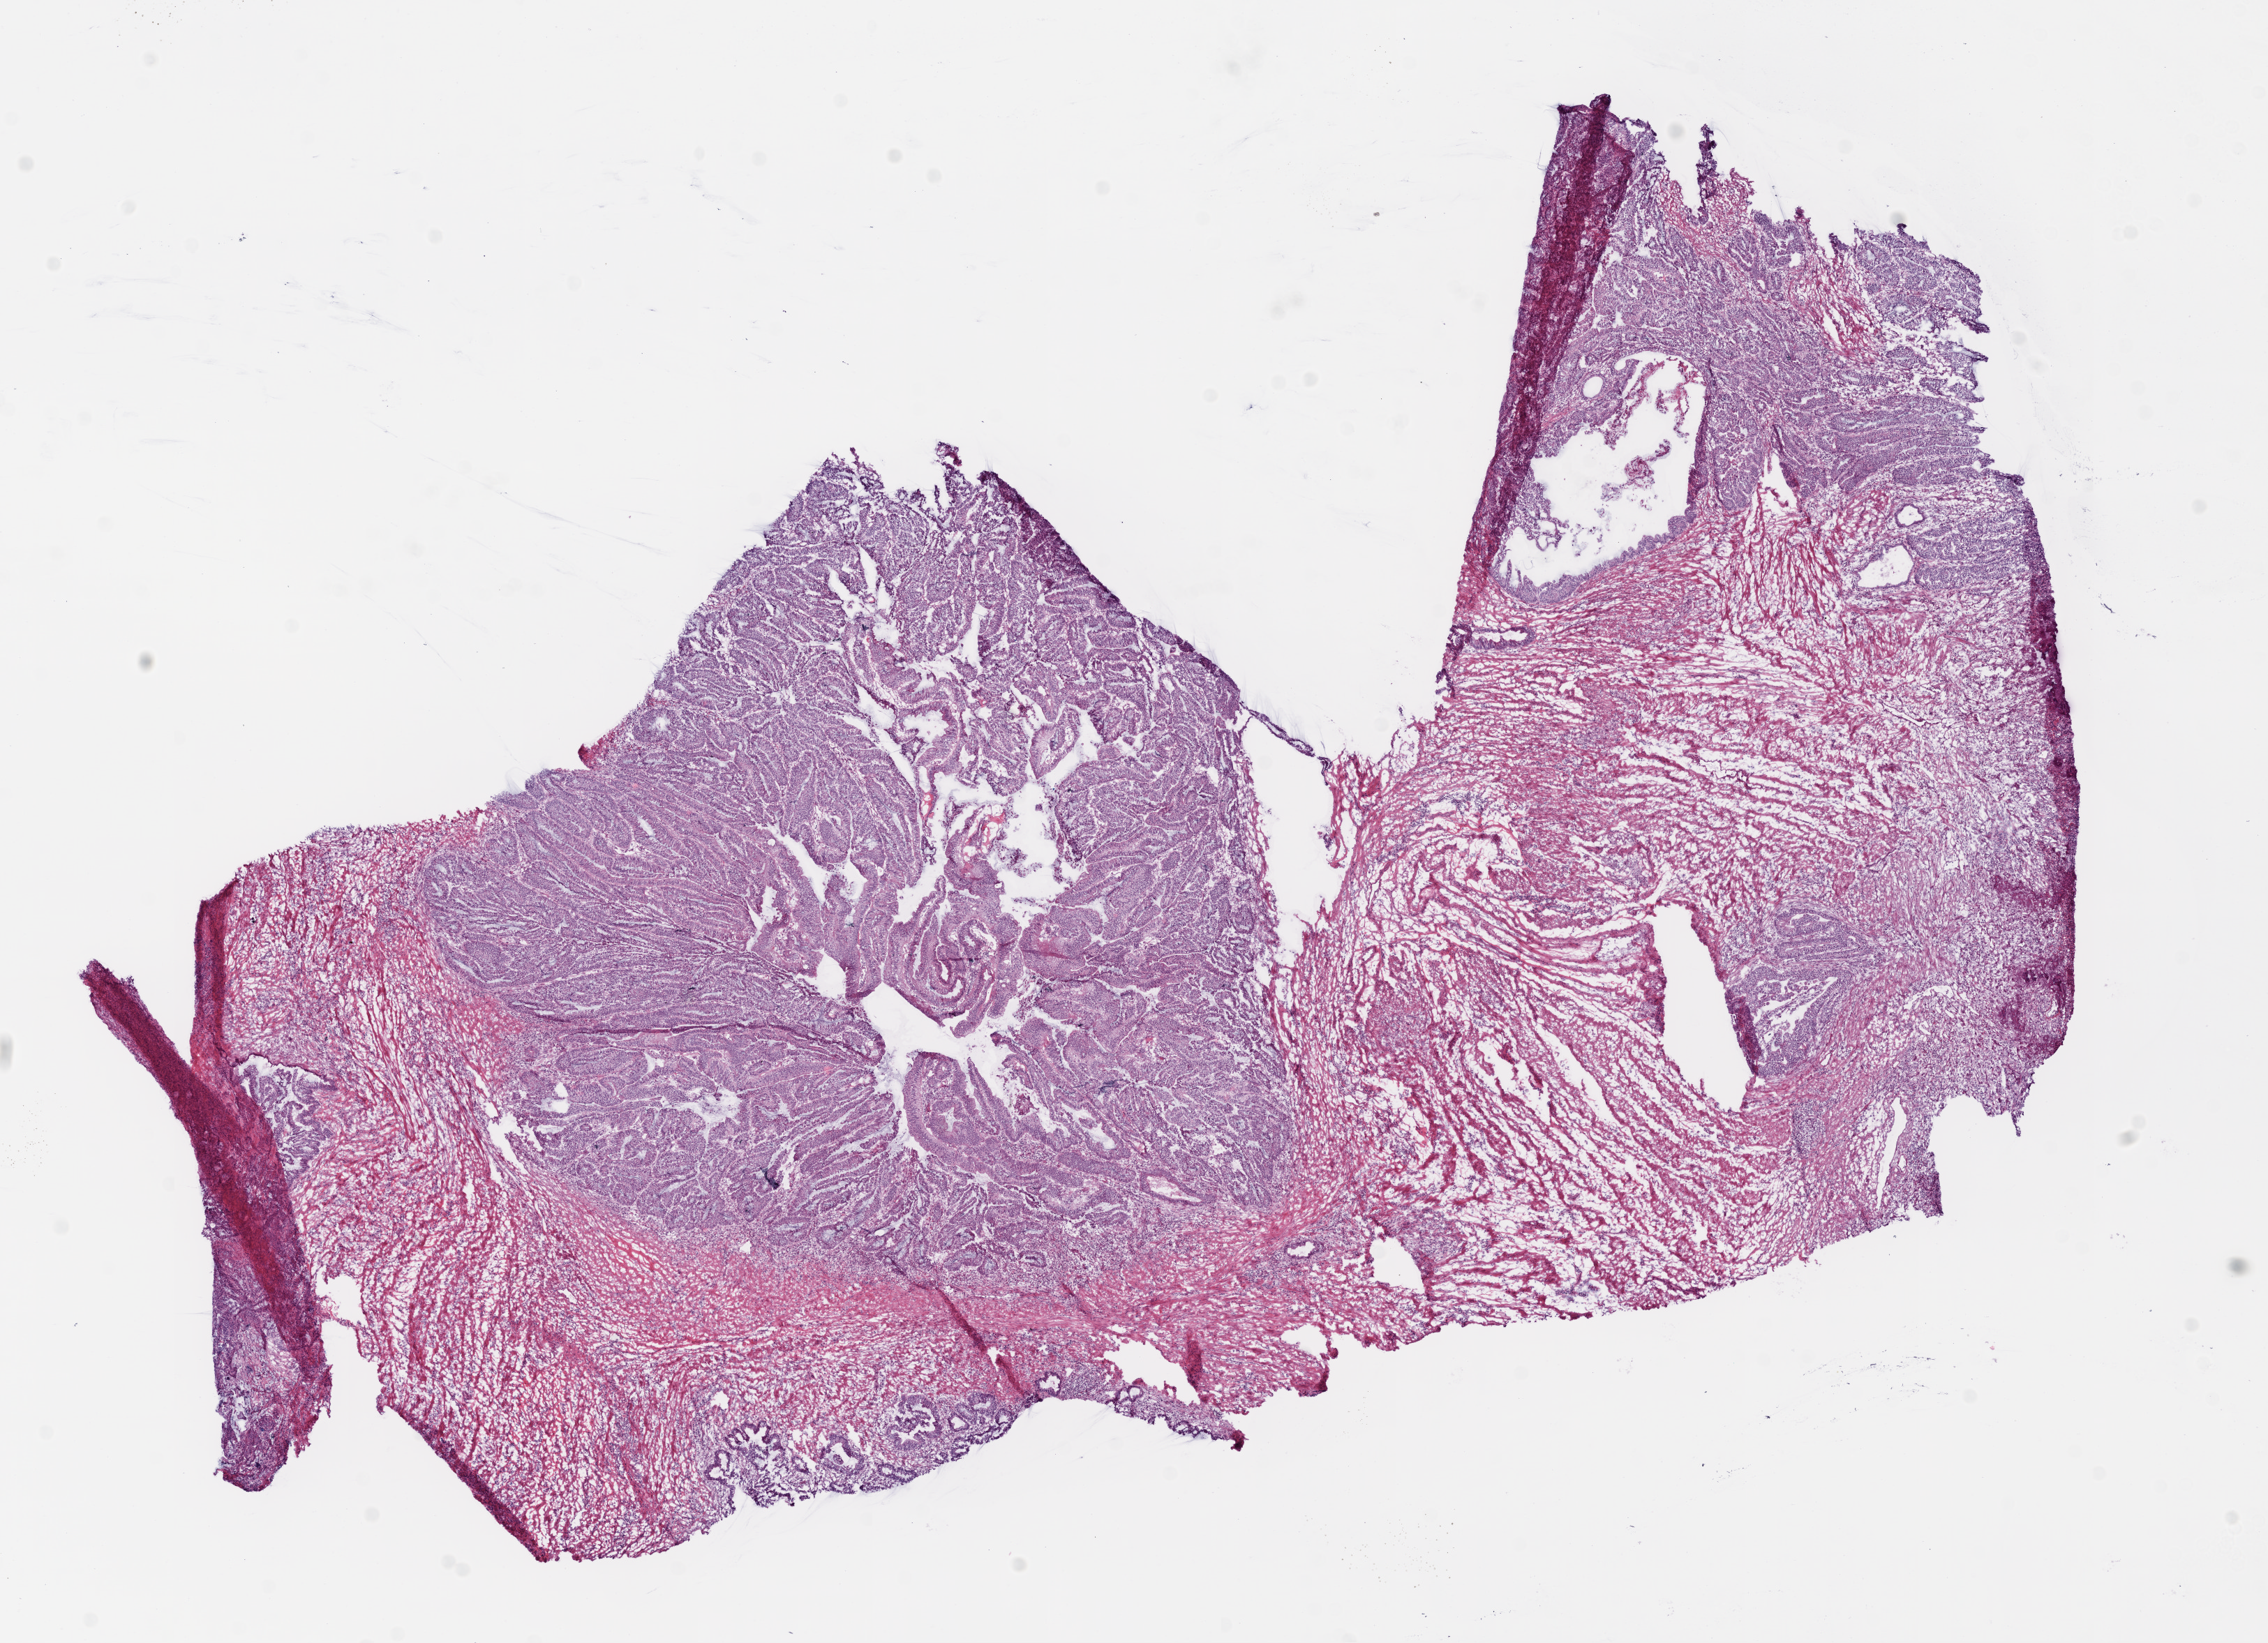
Whole-slide histology image, Hematoxylin and eosin (H&E) stained — low-resolution overview of the scanned area, about 13.0 x 9.4 mm; frozen section from the top of the tissue portion; colon, primary tumour sample. Patient: female, age at initial diagnosis 78 years. Composition of this section per pathologist review: tumour cells 65%, tumour nuclei 75%, normal cells 0%, stromal cells 30%, necrosis 5%.
AJCC pathologic stage: IIA. Histologic diagnosis: Adenocarcinoma, NOS. TNM: T3 N0 M0. Lymph nodes positive (case pathology): 0 of 18 examined.